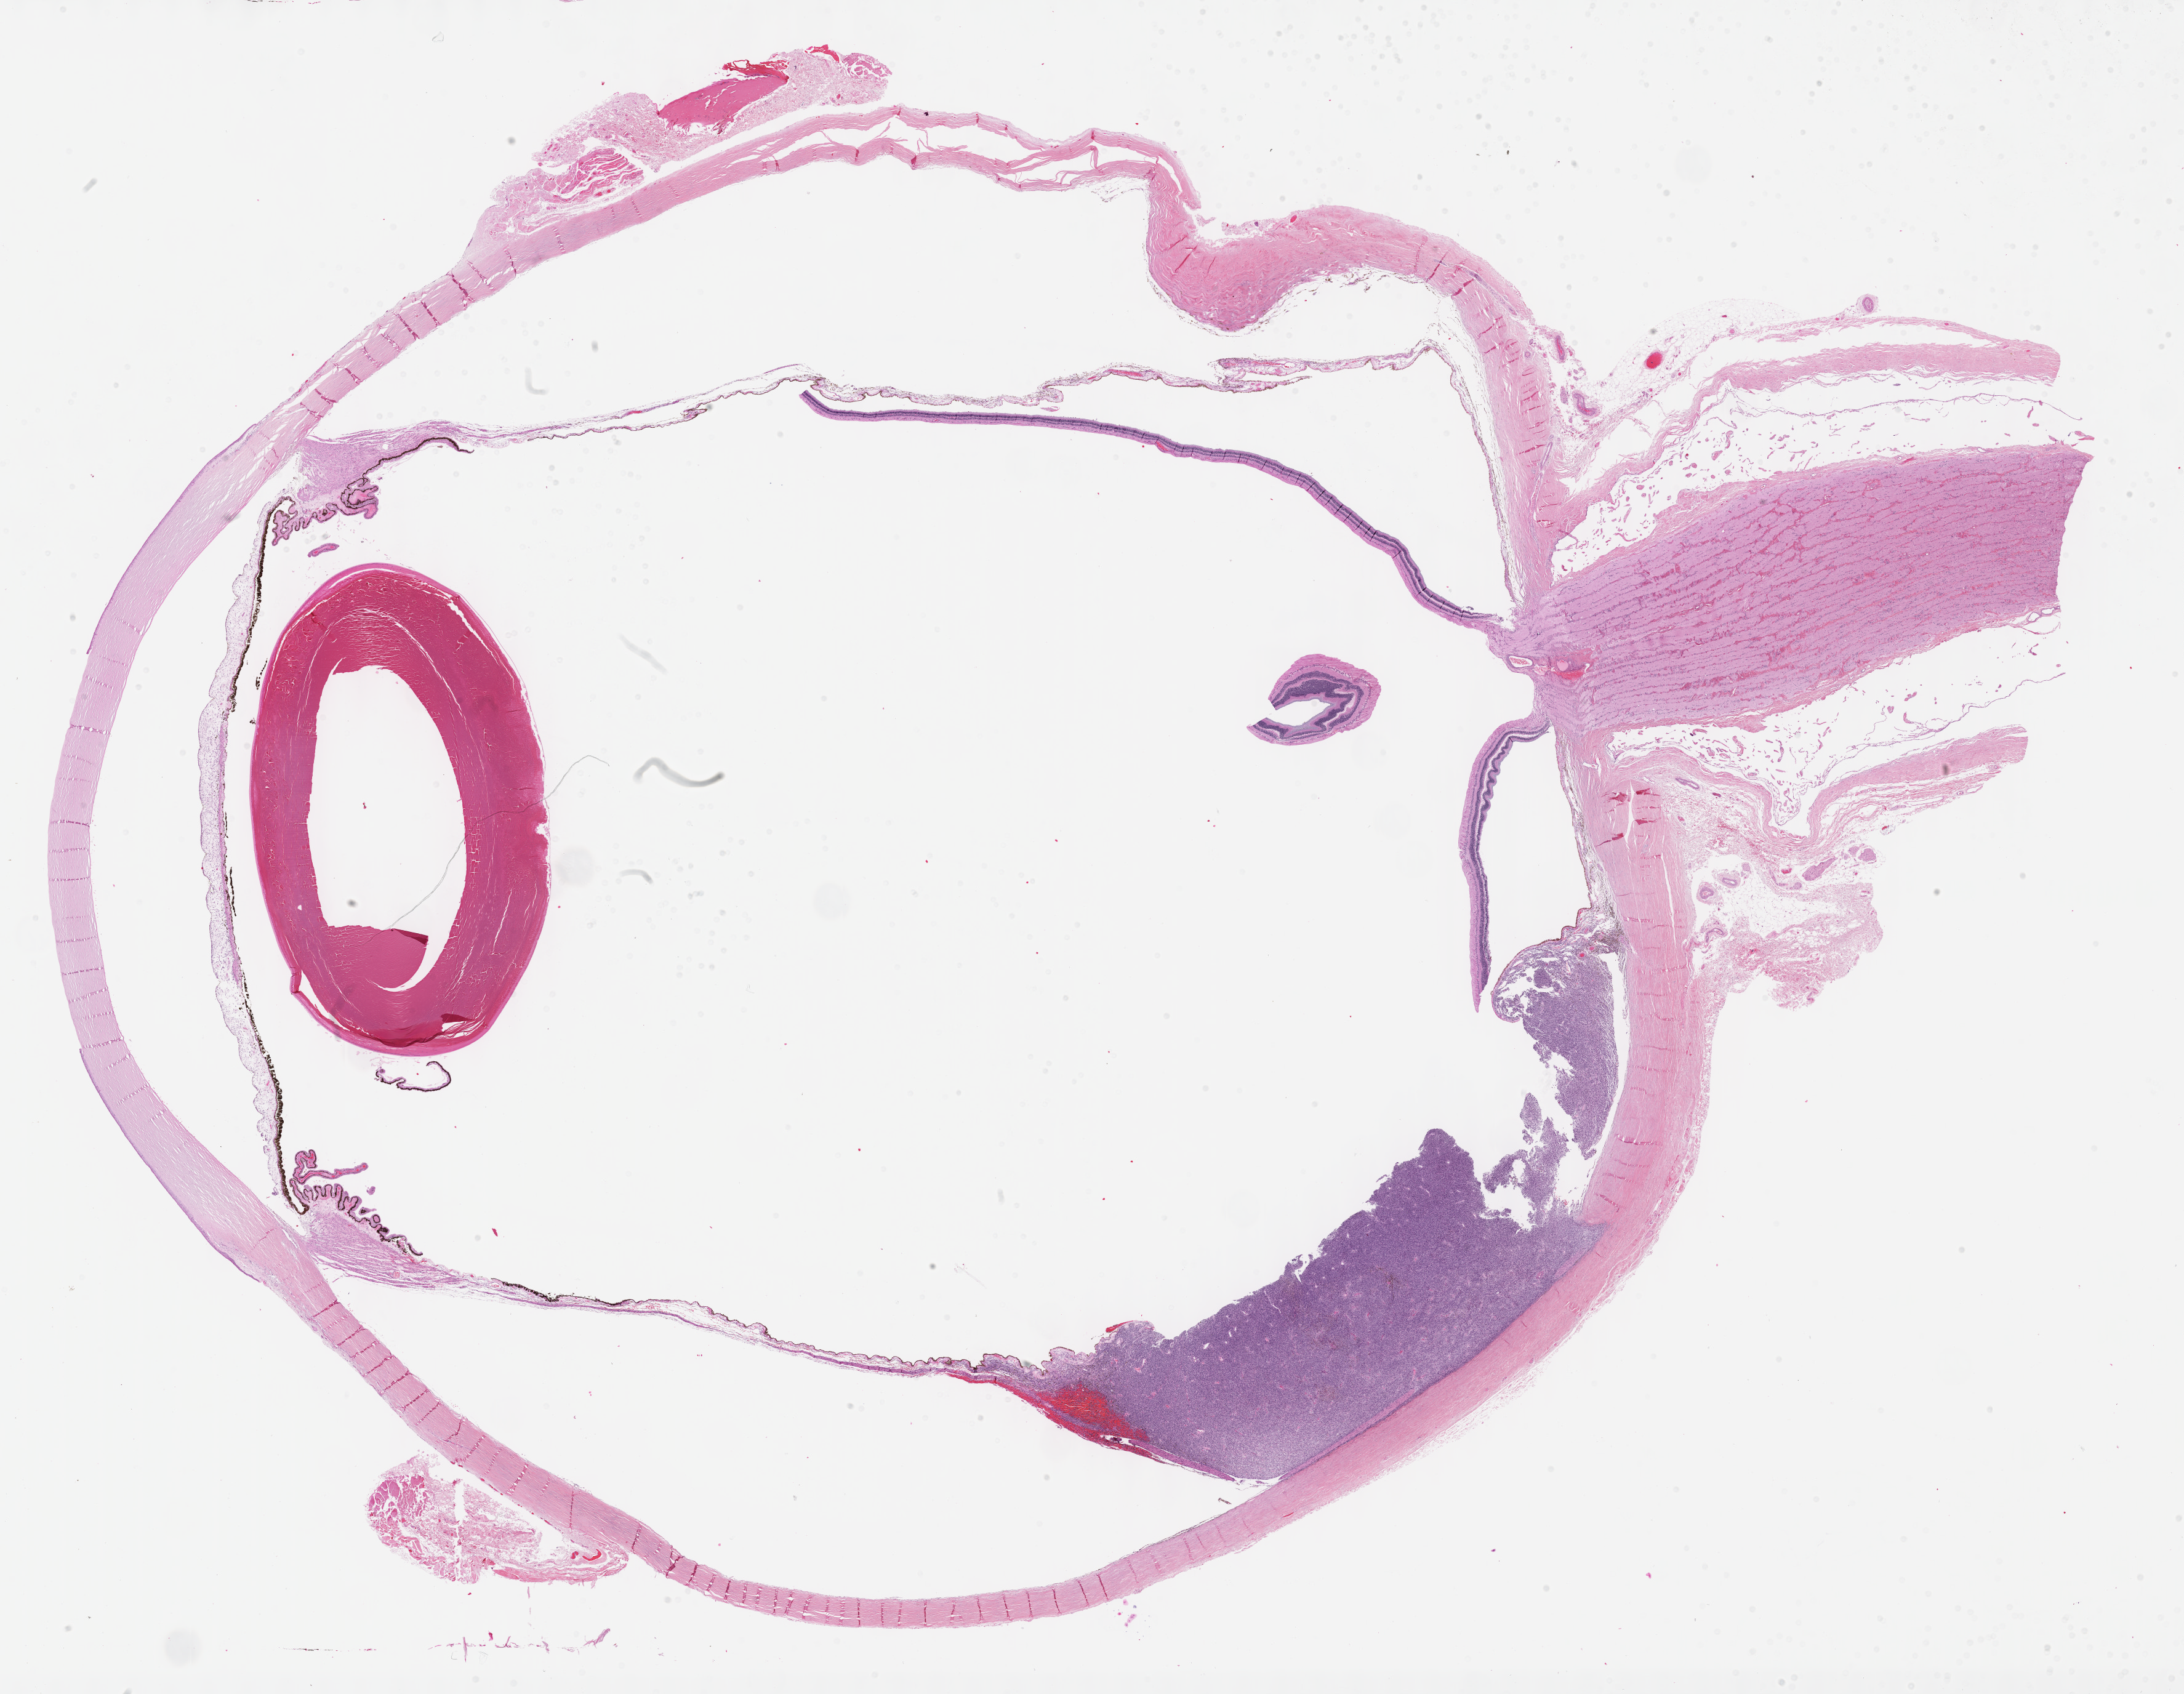
Hematoxylin and eosin (H&E) stained whole-slide image — shown as a low-resolution overview of the whole scanned area (about 28.7 x 22.3 mm, from a 40x scan). Formalin-fixed paraffin-embedded (FFPE) diagnostic section. Primary tumour sample from the uvea. Female patient; age at initial diagnosis 57 years.
Pathologic diagnosis: Spindle cell melanoma, NOS (choroid). Laterality: left. AJCC pathologic stage: IIA (7th edition).